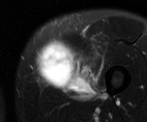
MRI of an extremity soft-tissue mass, one axial slice; T2-weighted fat-saturated; MR volume resampled by the dataset authors to the PET/CT grid (not the native acquisition matrix); 3.27 mm slice thickness; 147 × 122 image matrix, field of view 144 × 119 mm. Male patient. Case-level facts recorded for this patient, not image findings: histological type: pleiomorphic liposarcoma; grade: high; site of the primary tumour: left thigh.
Outlined on this slice (expert contour drawn on MRI and transferred to this co-registered scan by the dataset authors):
- gross tumour volume including surrounding oedema: bounding box [x1, y1, x2, y2] px = [34, 37, 101, 99]
- gross tumour volume (mass): [34, 37, 79, 90]